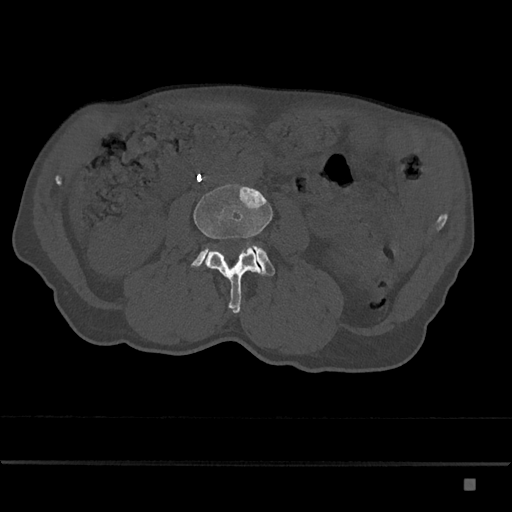
CT including the spine, one axial slice; 120 kVp; bone window (W 1800 / L 400 HU); 0.5 mm slice thickness; 512 × 512 image matrix, field of view 390 × 390 mm. Patient: male, 72 years. Case-level facts recorded for this patient, not image findings: primary cancer: prostate.
Annotated regions visible in this slice (semi-automatically segmented with operator editing):
- L3 vertebra: box from (x=194, y=184) to (x=273, y=313) px
- L4 vertebra: (x=192, y=244)–(x=275, y=276)